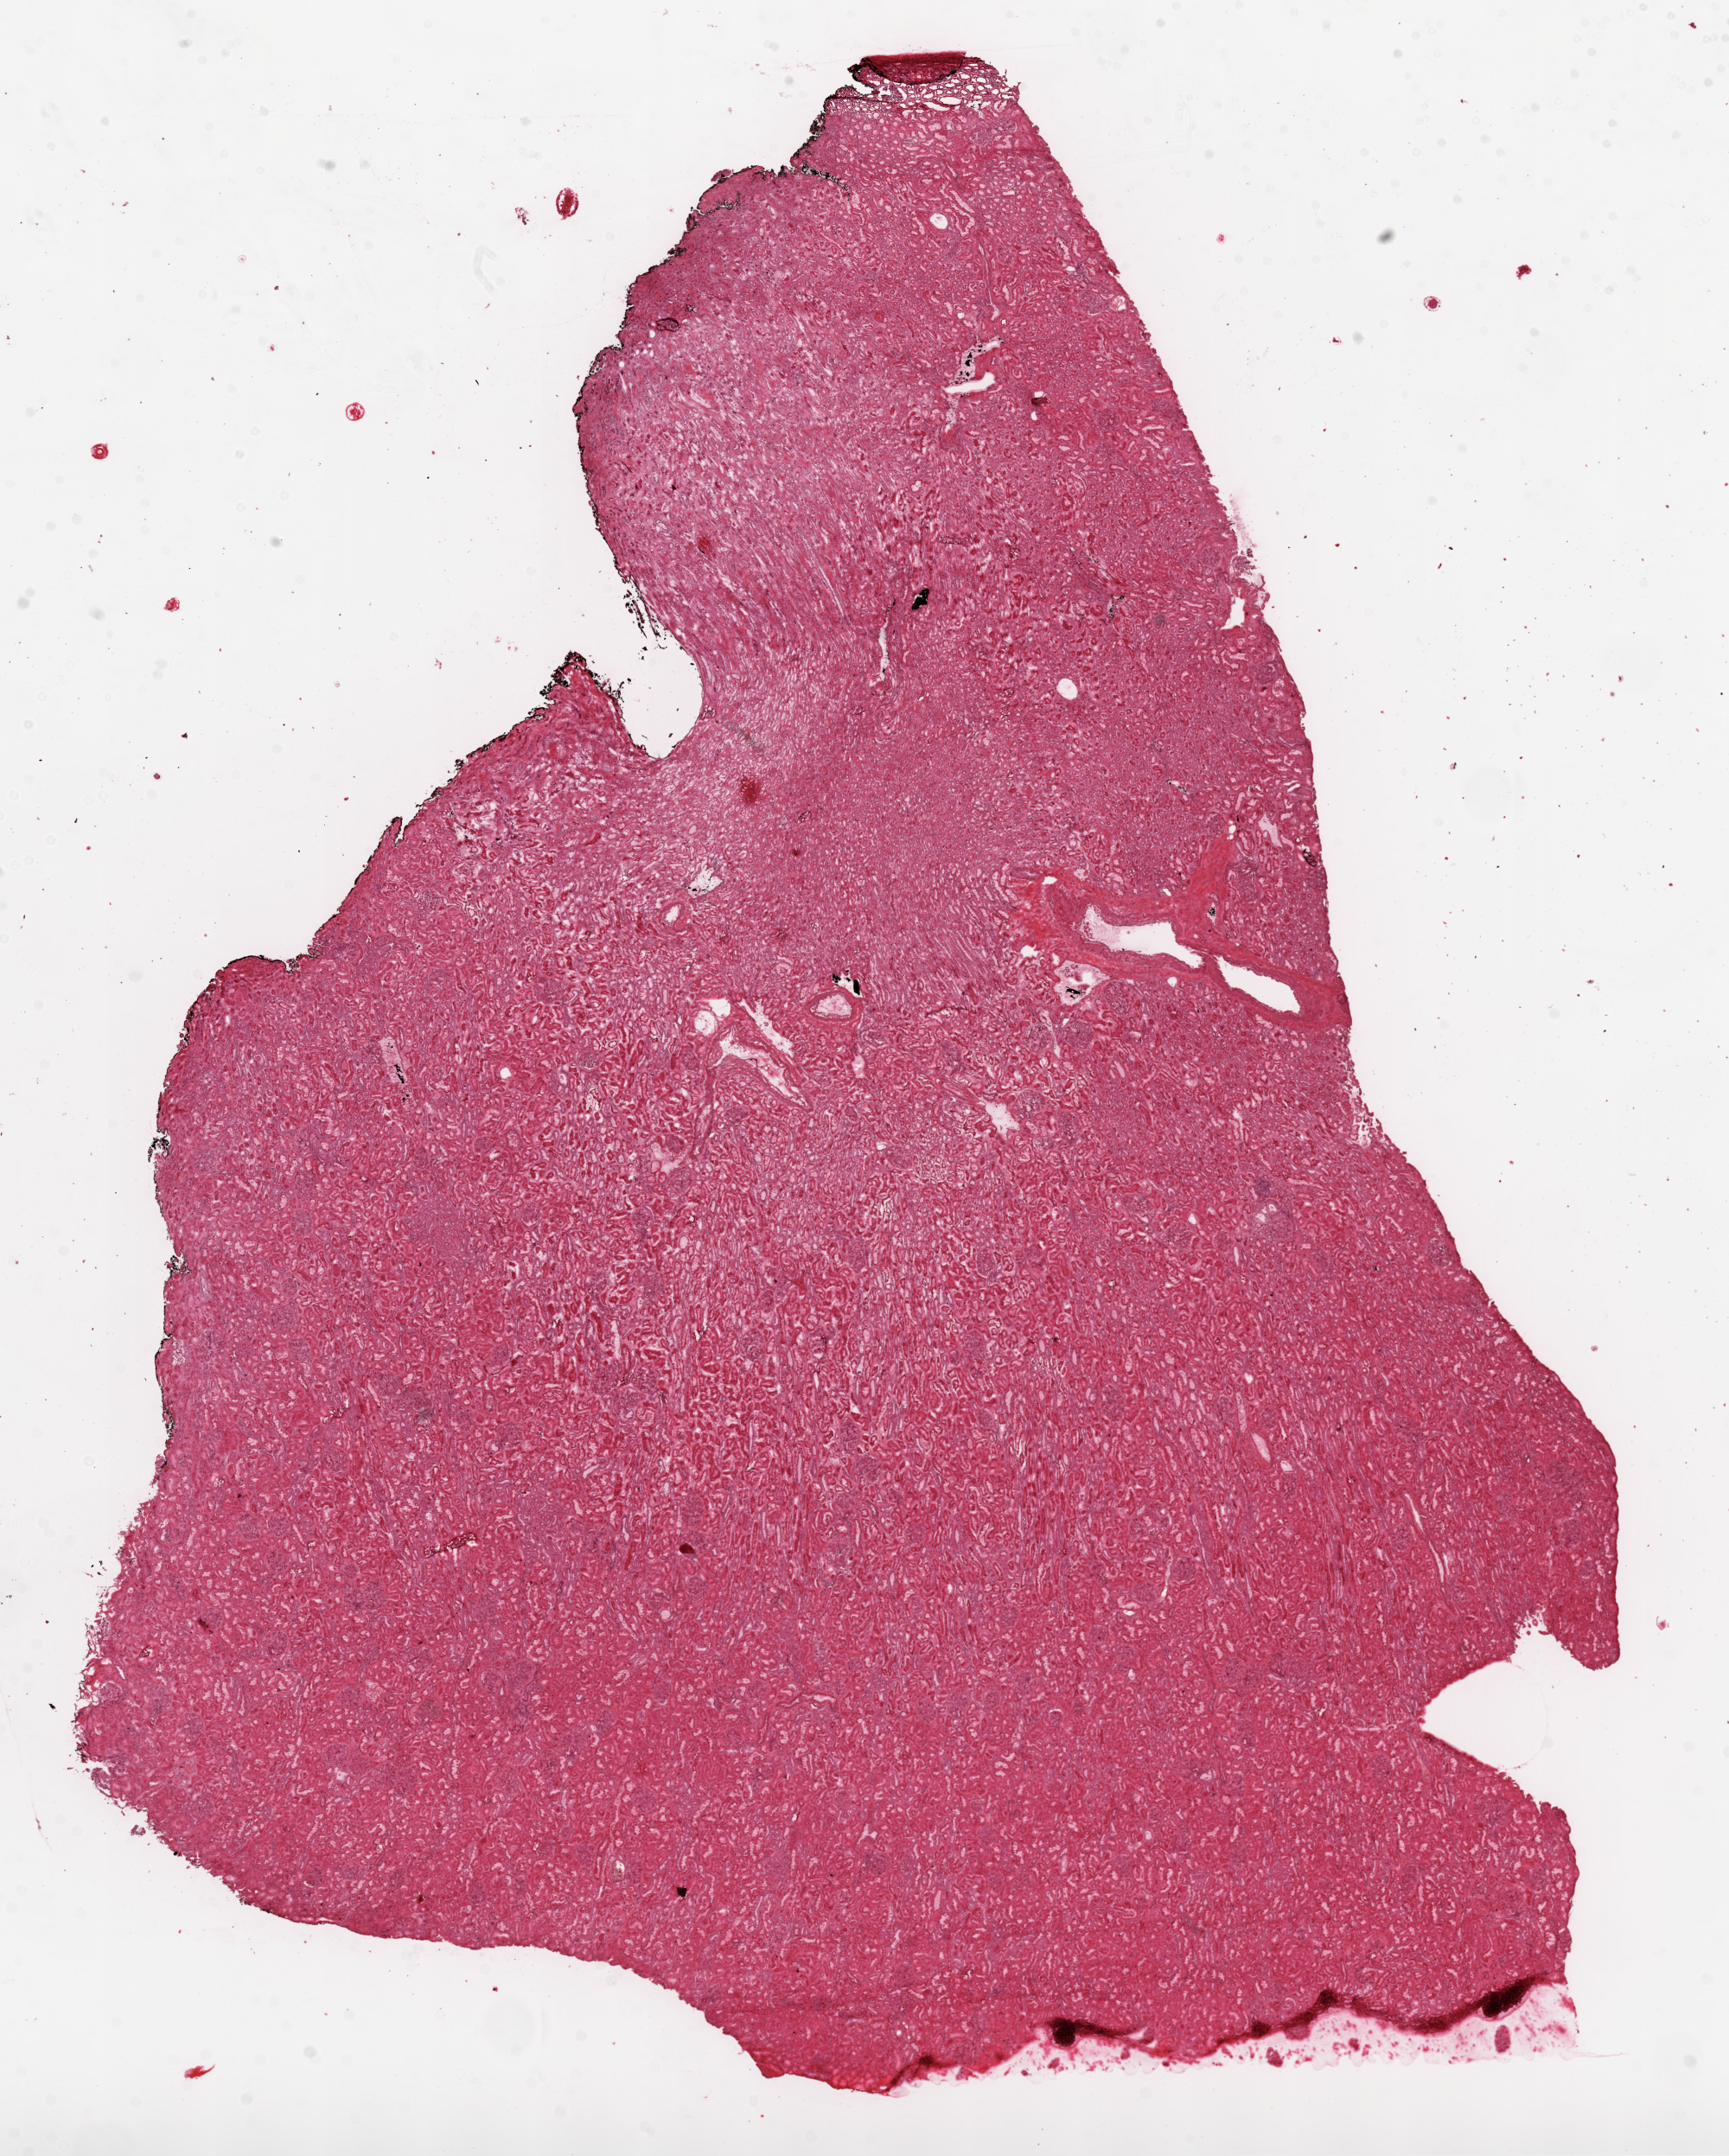
Digitized H&E-stained tissue section (whole slide), shown as a low-resolution overview of the whole scanned area (about 16.0 x 20.0 mm, from a 20x scan), frozen section, solid tissue normal (non-tumour tissue) sample from the kidney. Male patient; age at initial diagnosis 49 years.
• this section: solid tissue normal (non-tumour) sample from the same patient
• patient diagnosis: Clear cell adenocarcinoma, NOS